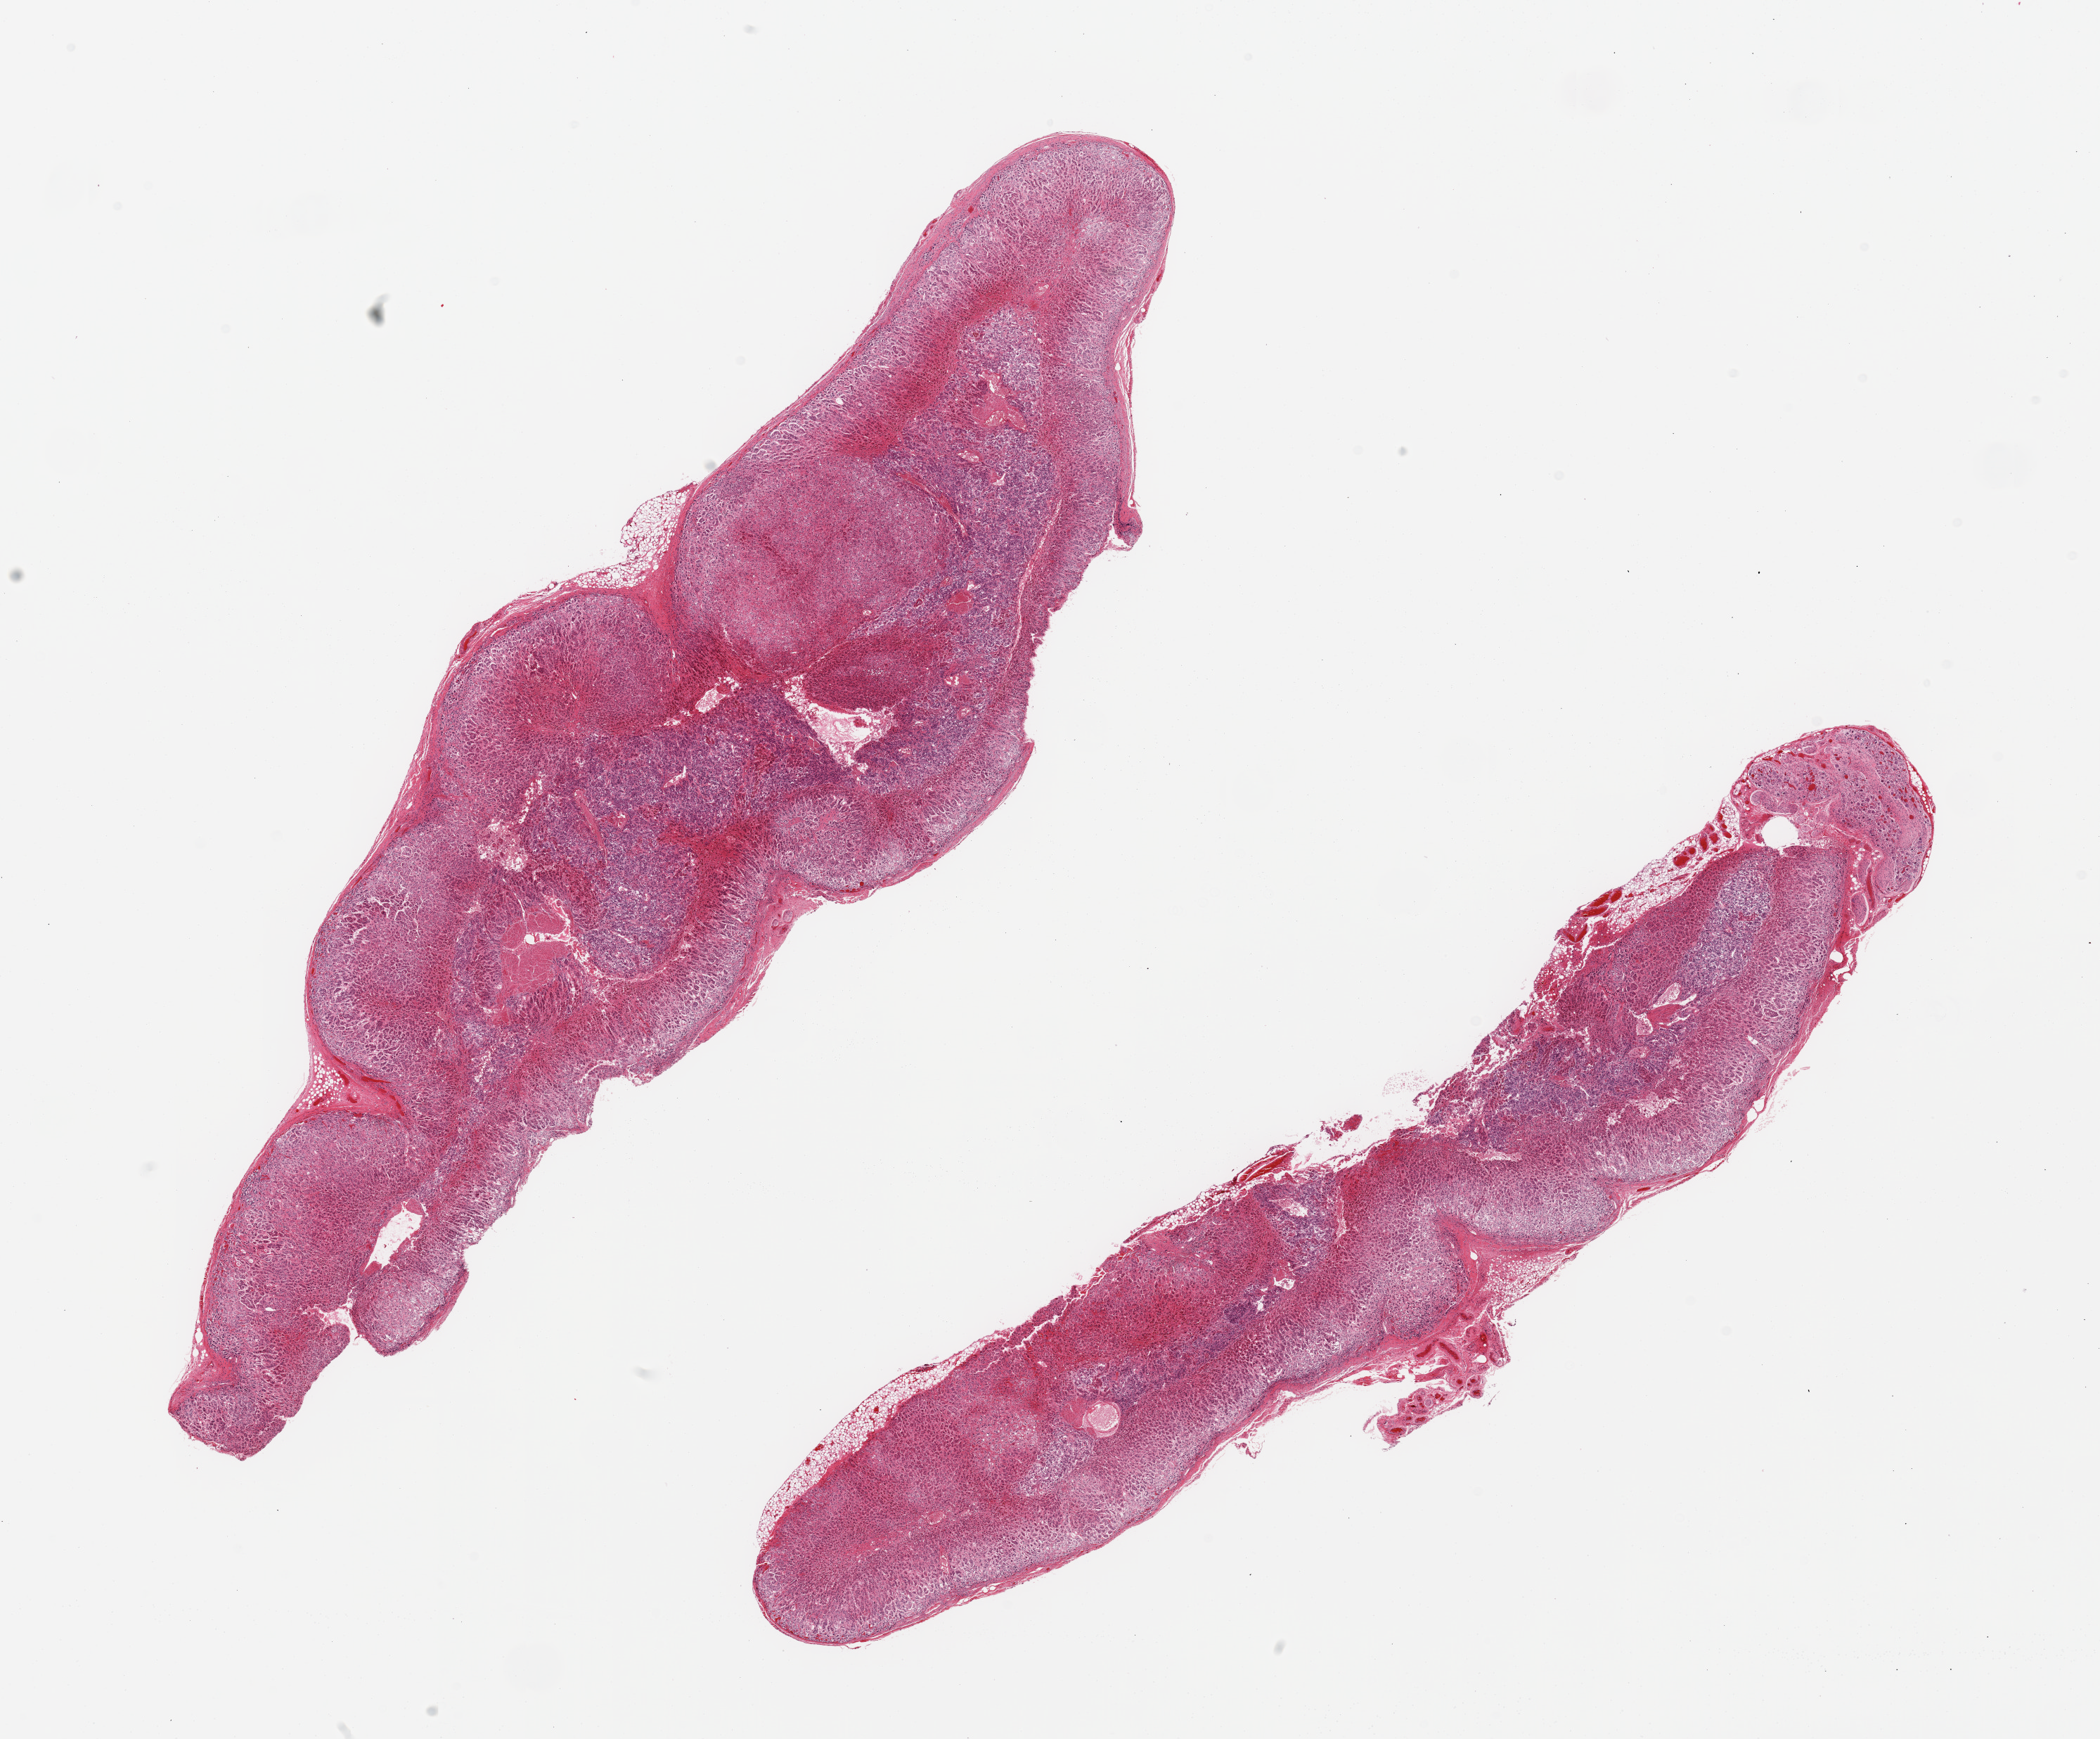
Whole-slide image, haematoxylin and eosin stain, brightfield — a low-resolution overview of the entire scanned area, about 23.6 x 19.6 mm (from a 20x scan), PAXgene-fixed paraffin-embedded (PFPE) section, target tissue: adrenal gland, donor tissue sample. Donor sex: female.
Review note (as recorded): 2 pieces; well trimmed; one includes portion of cortical nodule; cortex and medulla with central adrenal vein; one with attached nerves and ganglion.